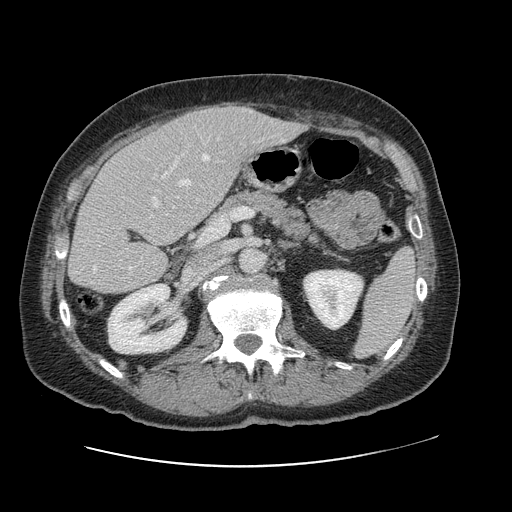
Contrast-enhanced abdominal CT, one axial slice; slice 53 of 138 in the series (ordered by position); 120 kVp; intravenous contrast given; soft-tissue window (W 400 / L 40 HU); 2.5 mm slice thickness; 512 × 512 image matrix. Male patient, age 71 years. Case-level facts recorded for this patient, not image findings: diagnosis: colorectal cancer liver metastases, imaged before liver resection; multiple liver metastases: no; largest metastasis: 3.3 cm.
Annotated regions visible in this slice (outlined manually by an expert reader):
- hepatic veins: bounding box [x1, y1, x2, y2] px = [93, 155, 227, 273]
- liver: [70, 105, 300, 294]
- planned liver remnant (the part of the liver to remain after resection): [70, 142, 199, 294]
- portal vein (with intrahepatic branches): [152, 171, 169, 208]